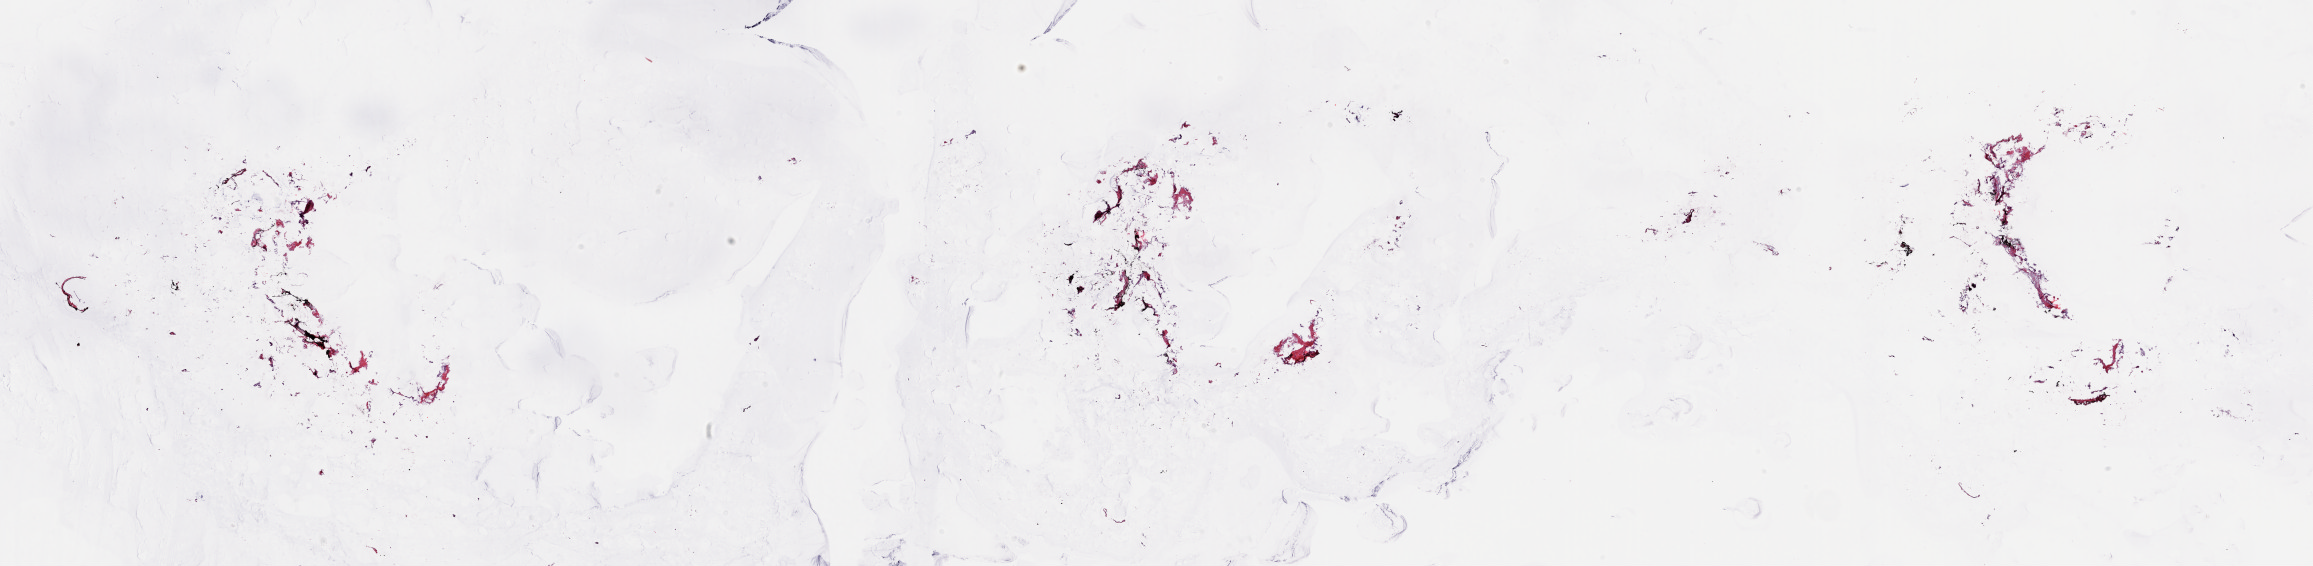
Digitized H&E tissue section (whole slide), a low-resolution overview of the entire scanned area, about 36.7 x 9.0 mm (acquisition: 20x scan), frozen section, solid tissue normal (non-tumour tissue) sample from the breast. Female, age 54 years at initial diagnosis. Pathologist review of this section (percent, as recorded): tumour cells 0%, tumour nuclei 0%, normal cells 0%, stromal cells 100%, necrosis 0%. Inflammatory infiltration, as recorded: lymphocyte infiltration 0%, monocyte infiltration 0%, neutrophil infiltration 0%.
- this section: solid tissue normal sample (biorepository sample class)
- patient diagnosis: Infiltrating duct carcinoma, NOS